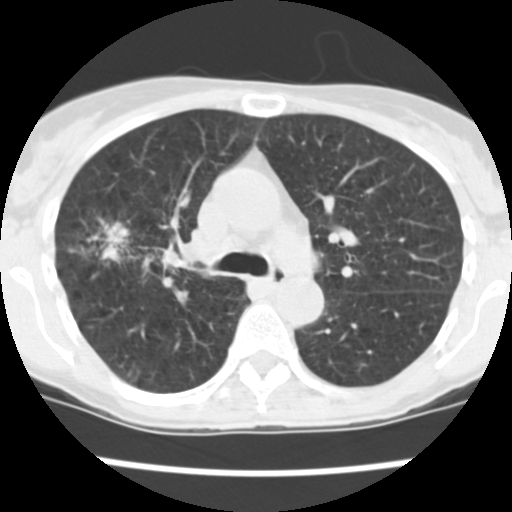
Axial slice from a low-dose chest CT screening exam. Baseline annual screen. Lung window (W 1500 / L -600 HU). Slice 161 of 252 in the series. Female, age 60 years at enrolment. Current smoker at enrolment.
Expert reader's lesion annotation, bounding box (x1, y1, x2, y2) in pixels: (81, 216, 188, 282). The screening reader recorded 3 non-calcified nodules or masses ≥4 mm on this exam (right upper lobe, right upper lobe, right lower lobe); which of them this box marks is not recorded. Official screen result: positive, change unspecified: nodule(s) >= 4 mm or enlarging nodule(s), mass(es), or other non-specific abnormalities suspicious for lung cancer. Participant outcome: lung cancer diagnosed 19 days after this screen — non-small cell carcinoma, right upper lobe, stage IV (AJCC 6th edition), 26 mm at pathology.